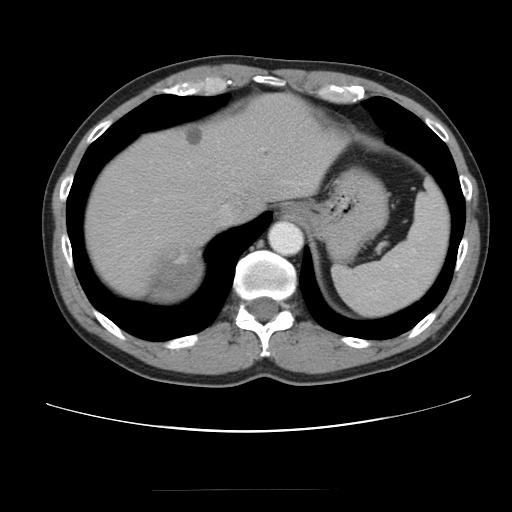
Contrast-enhanced abdominal CT, one axial slice; slice 72 of 80 in the series (ordered by position); reconstruction kernel STANDARD; 120 kVp; intravenous contrast given; soft-tissue window (W 400 / L 40 HU); 512 × 512 image matrix. Male patient, age 61 years. From the clinical record (not read from this slice): diagnosis: adrenocortical carcinoma; tumour side: right adrenal; tumour size at pathology: 11.1 cm; Ki-67 index: 32 %; stage (as recorded): 2.
Structures marked on this image (semi-automatic segmentation, software-assisted and operator-edited):
- mass: bounding box (x1, y1, x2, y2) in pixels: (149, 243, 200, 296)